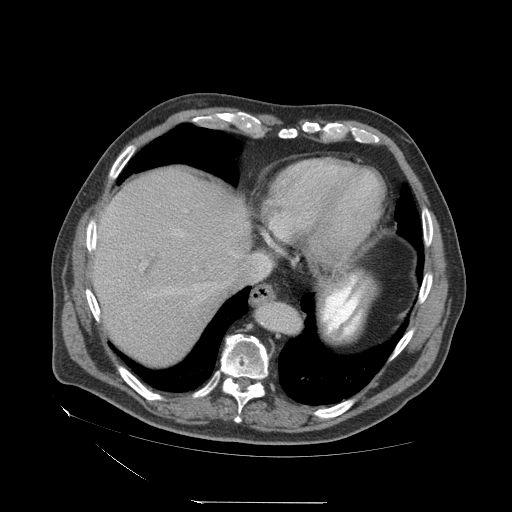
Contrast-enhanced abdominal CT (liver protocol), one axial slice. Position 60 of 83 along the scan axis. Reconstruction kernel STANDARD. Soft-tissue window (W 400 / L 40 HU). 2.5 mm slice thickness. 512 × 512 image matrix, field of view 460 × 460 mm. Case-level facts recorded for this patient, not image findings: diagnosis: hepatocellular carcinoma (patient treated with transarterial chemoembolisation; whether this scan precedes or follows treatment is not stated here); TNM stage (as recorded): Stage-I; Child-Pugh class: A; tumour differentiation: well differentiated; tumour nodularity: uninodular.
Structures marked on this image (semi-automatically segmented with operator editing):
- abdominal aorta: bounding box <259,303,300,335> (left, top, right, bottom; pixels)
- liver parenchyma outside the tumour (the mass and vessels are separate outlines, so this box may not span the whole liver): <92,168,268,364>
- liver vessels: <154,235,237,296>